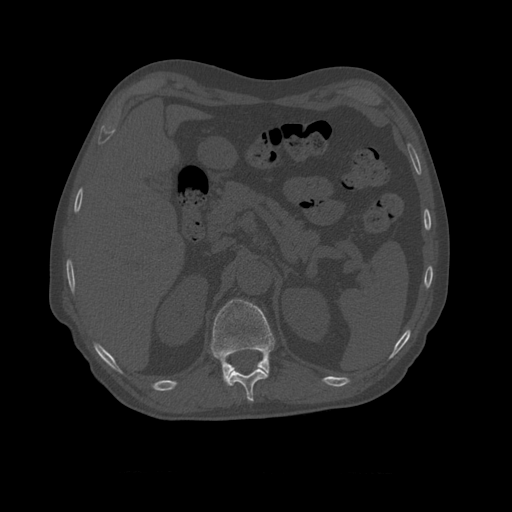
CT including the spine, one axial slice. Slice 390 of 450 in the series (ordered by position). Reconstruction kernel STANDARD. 120 kVp. Bone window (W 1800 / L 400 HU). 512 × 512 image matrix, field of view 405 × 405 mm. Patient age 75 years. From the clinical record (not read from this slice): primary cancer: prostate.
Structures marked on this image (semi-automatic segmentation, software-assisted and operator-edited):
- T10 vertebra: box from (x=227, y=368) to (x=269, y=402) px
- T11 vertebra: (x=211, y=299)–(x=275, y=385)